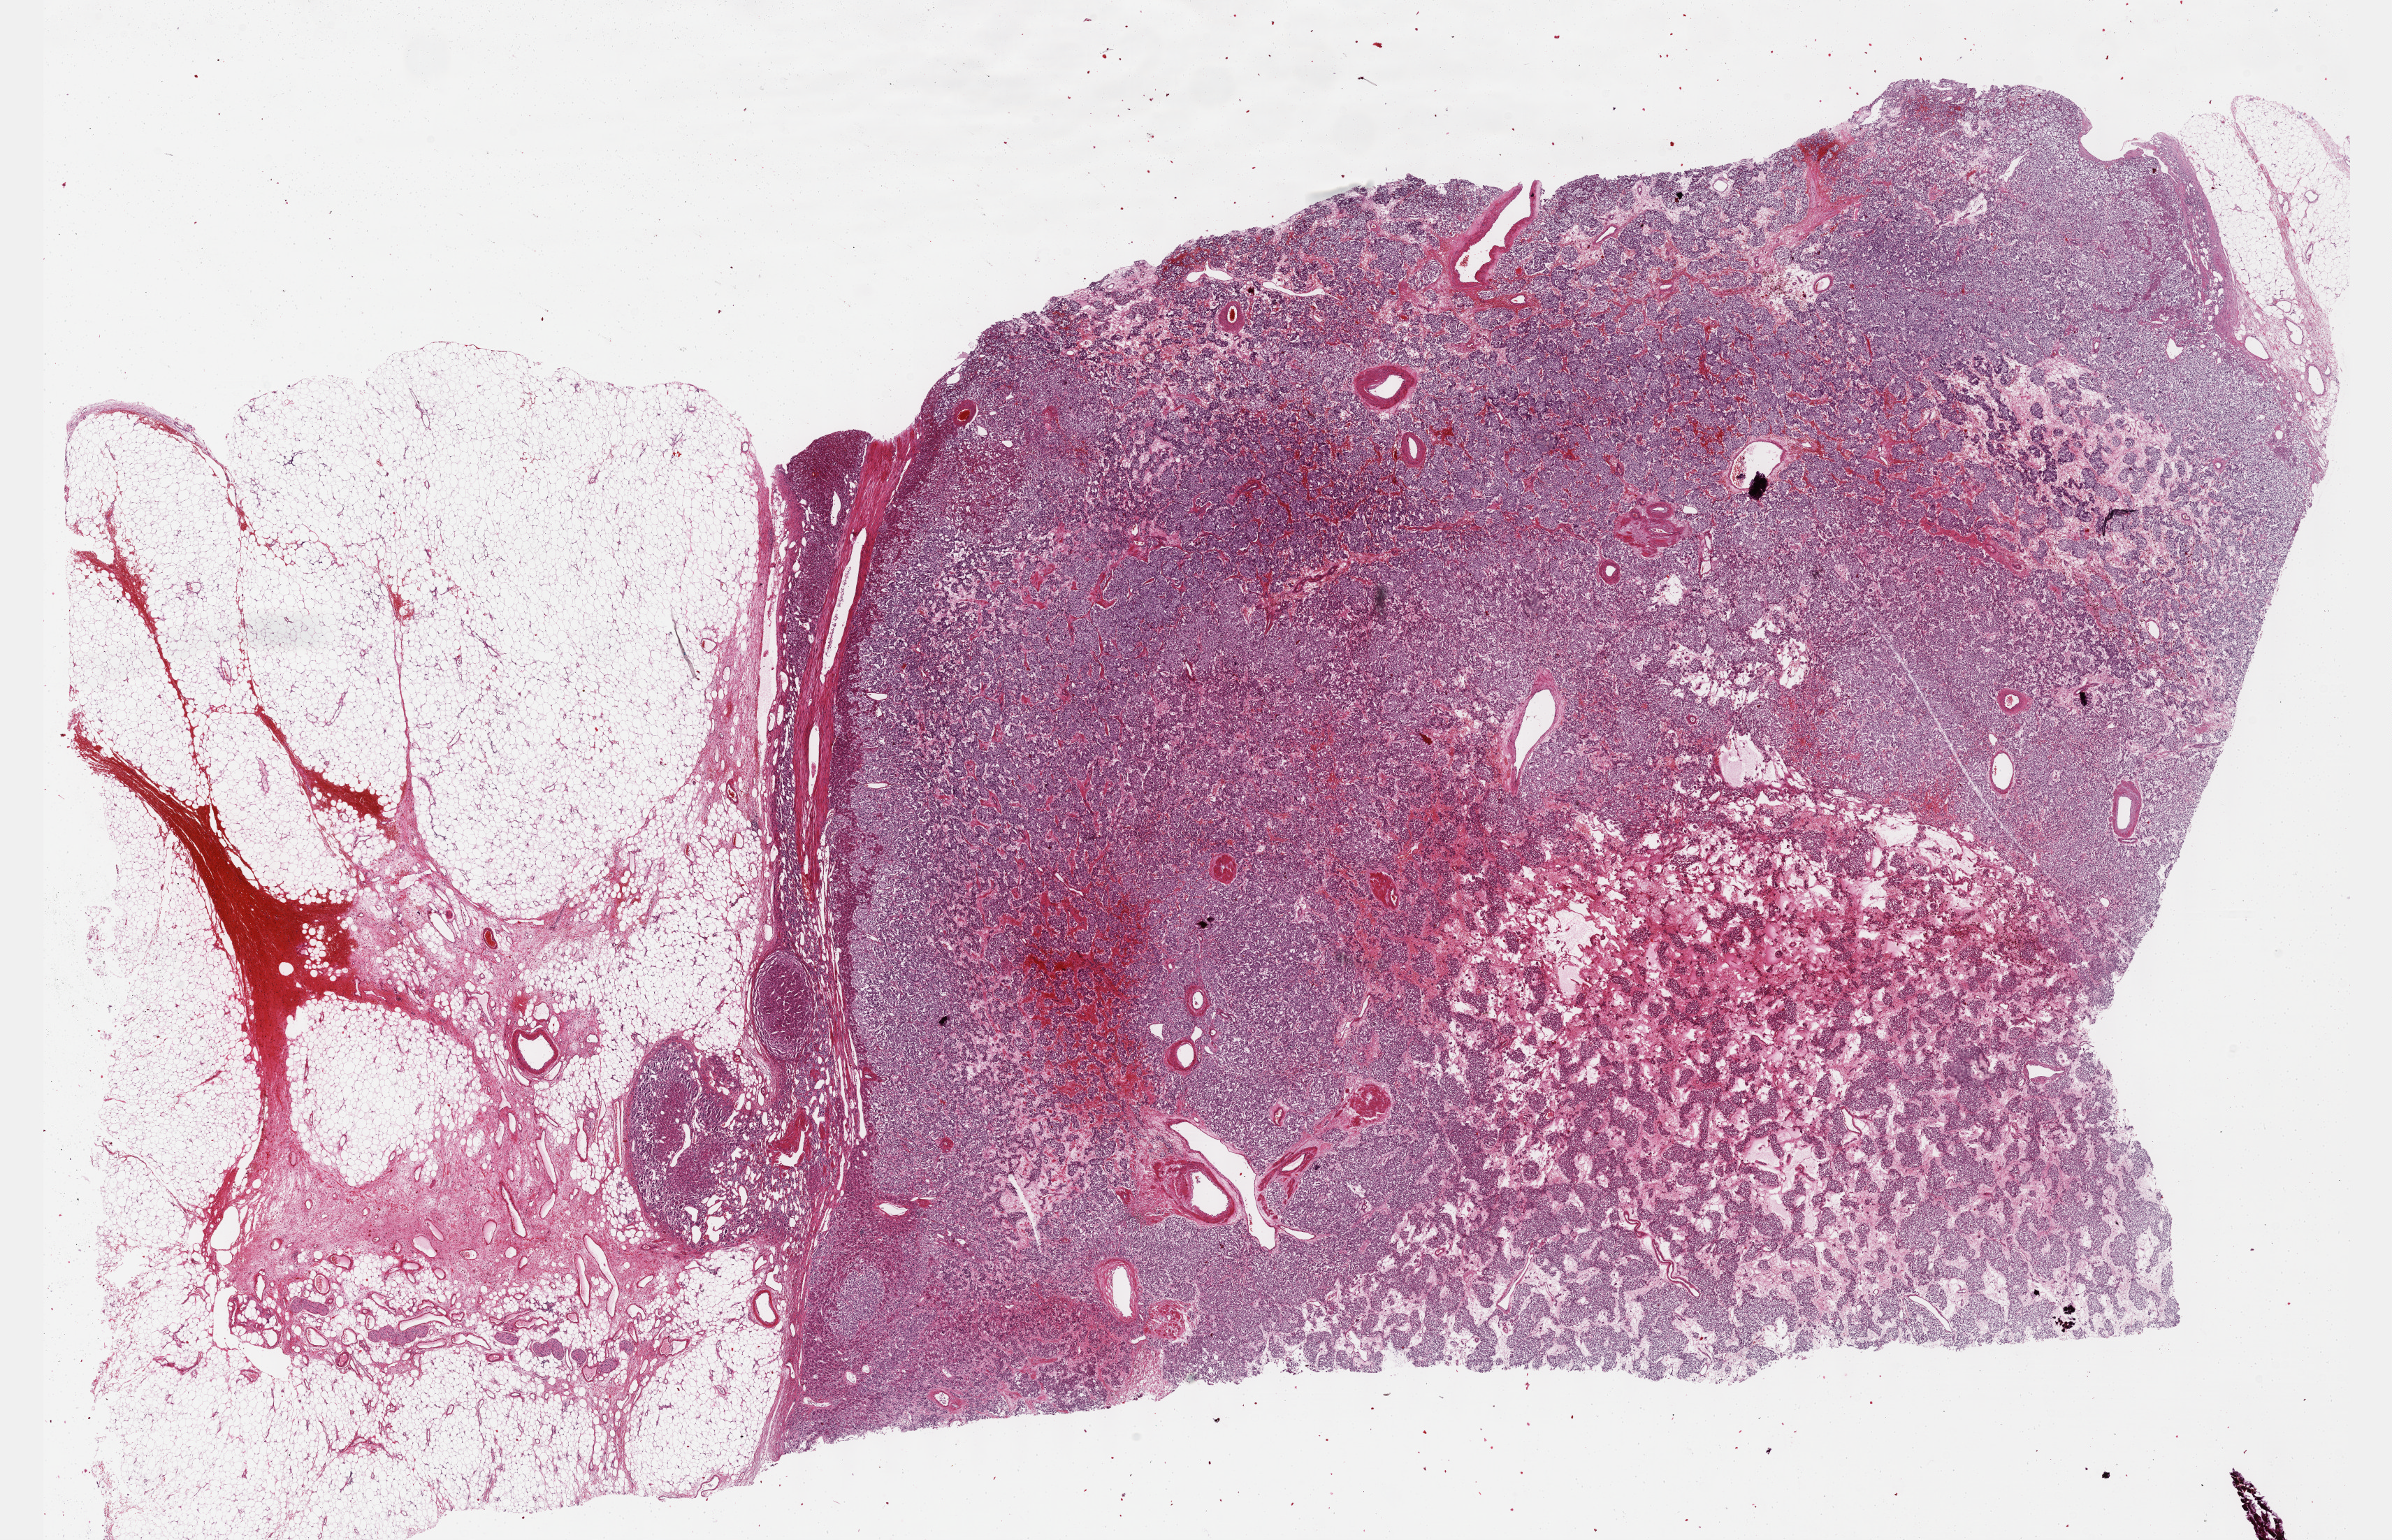
Whole-slide histology image, Hematoxylin and eosin (H&E) stained, whole scanned area (about 27.7 x 17.8 mm, from a 40x scan) shown as a low-resolution overview, formalin-fixed paraffin-embedded (FFPE) diagnostic section, primary tumour sample from the adrenal gland. Female patient; age at initial diagnosis 64 years.
Laterality: left. Diagnosis: Pheochromocytoma, malignant. Lymph nodes positive (case pathology): 1 of 1 examined.